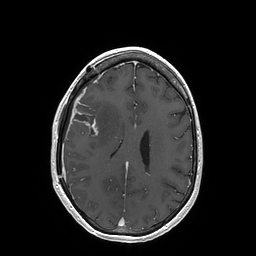
Brain MRI from a brain-tumour surgery series, one axial slice; position 66 of 202 along the scan axis; T1-weighted post-contrast; 1 mm slice thickness; 256 × 256 image matrix, field of view 250 × 250 mm. From the clinical record (not read from this slice): histopathology: Glioblastoma; WHO grade: 4; IDH mutation: no.
Annotated regions visible in this slice (manually delineated by an expert):
- tumour: bounding box (x1, y1, x2, y2) in pixels: (72, 108, 97, 136)